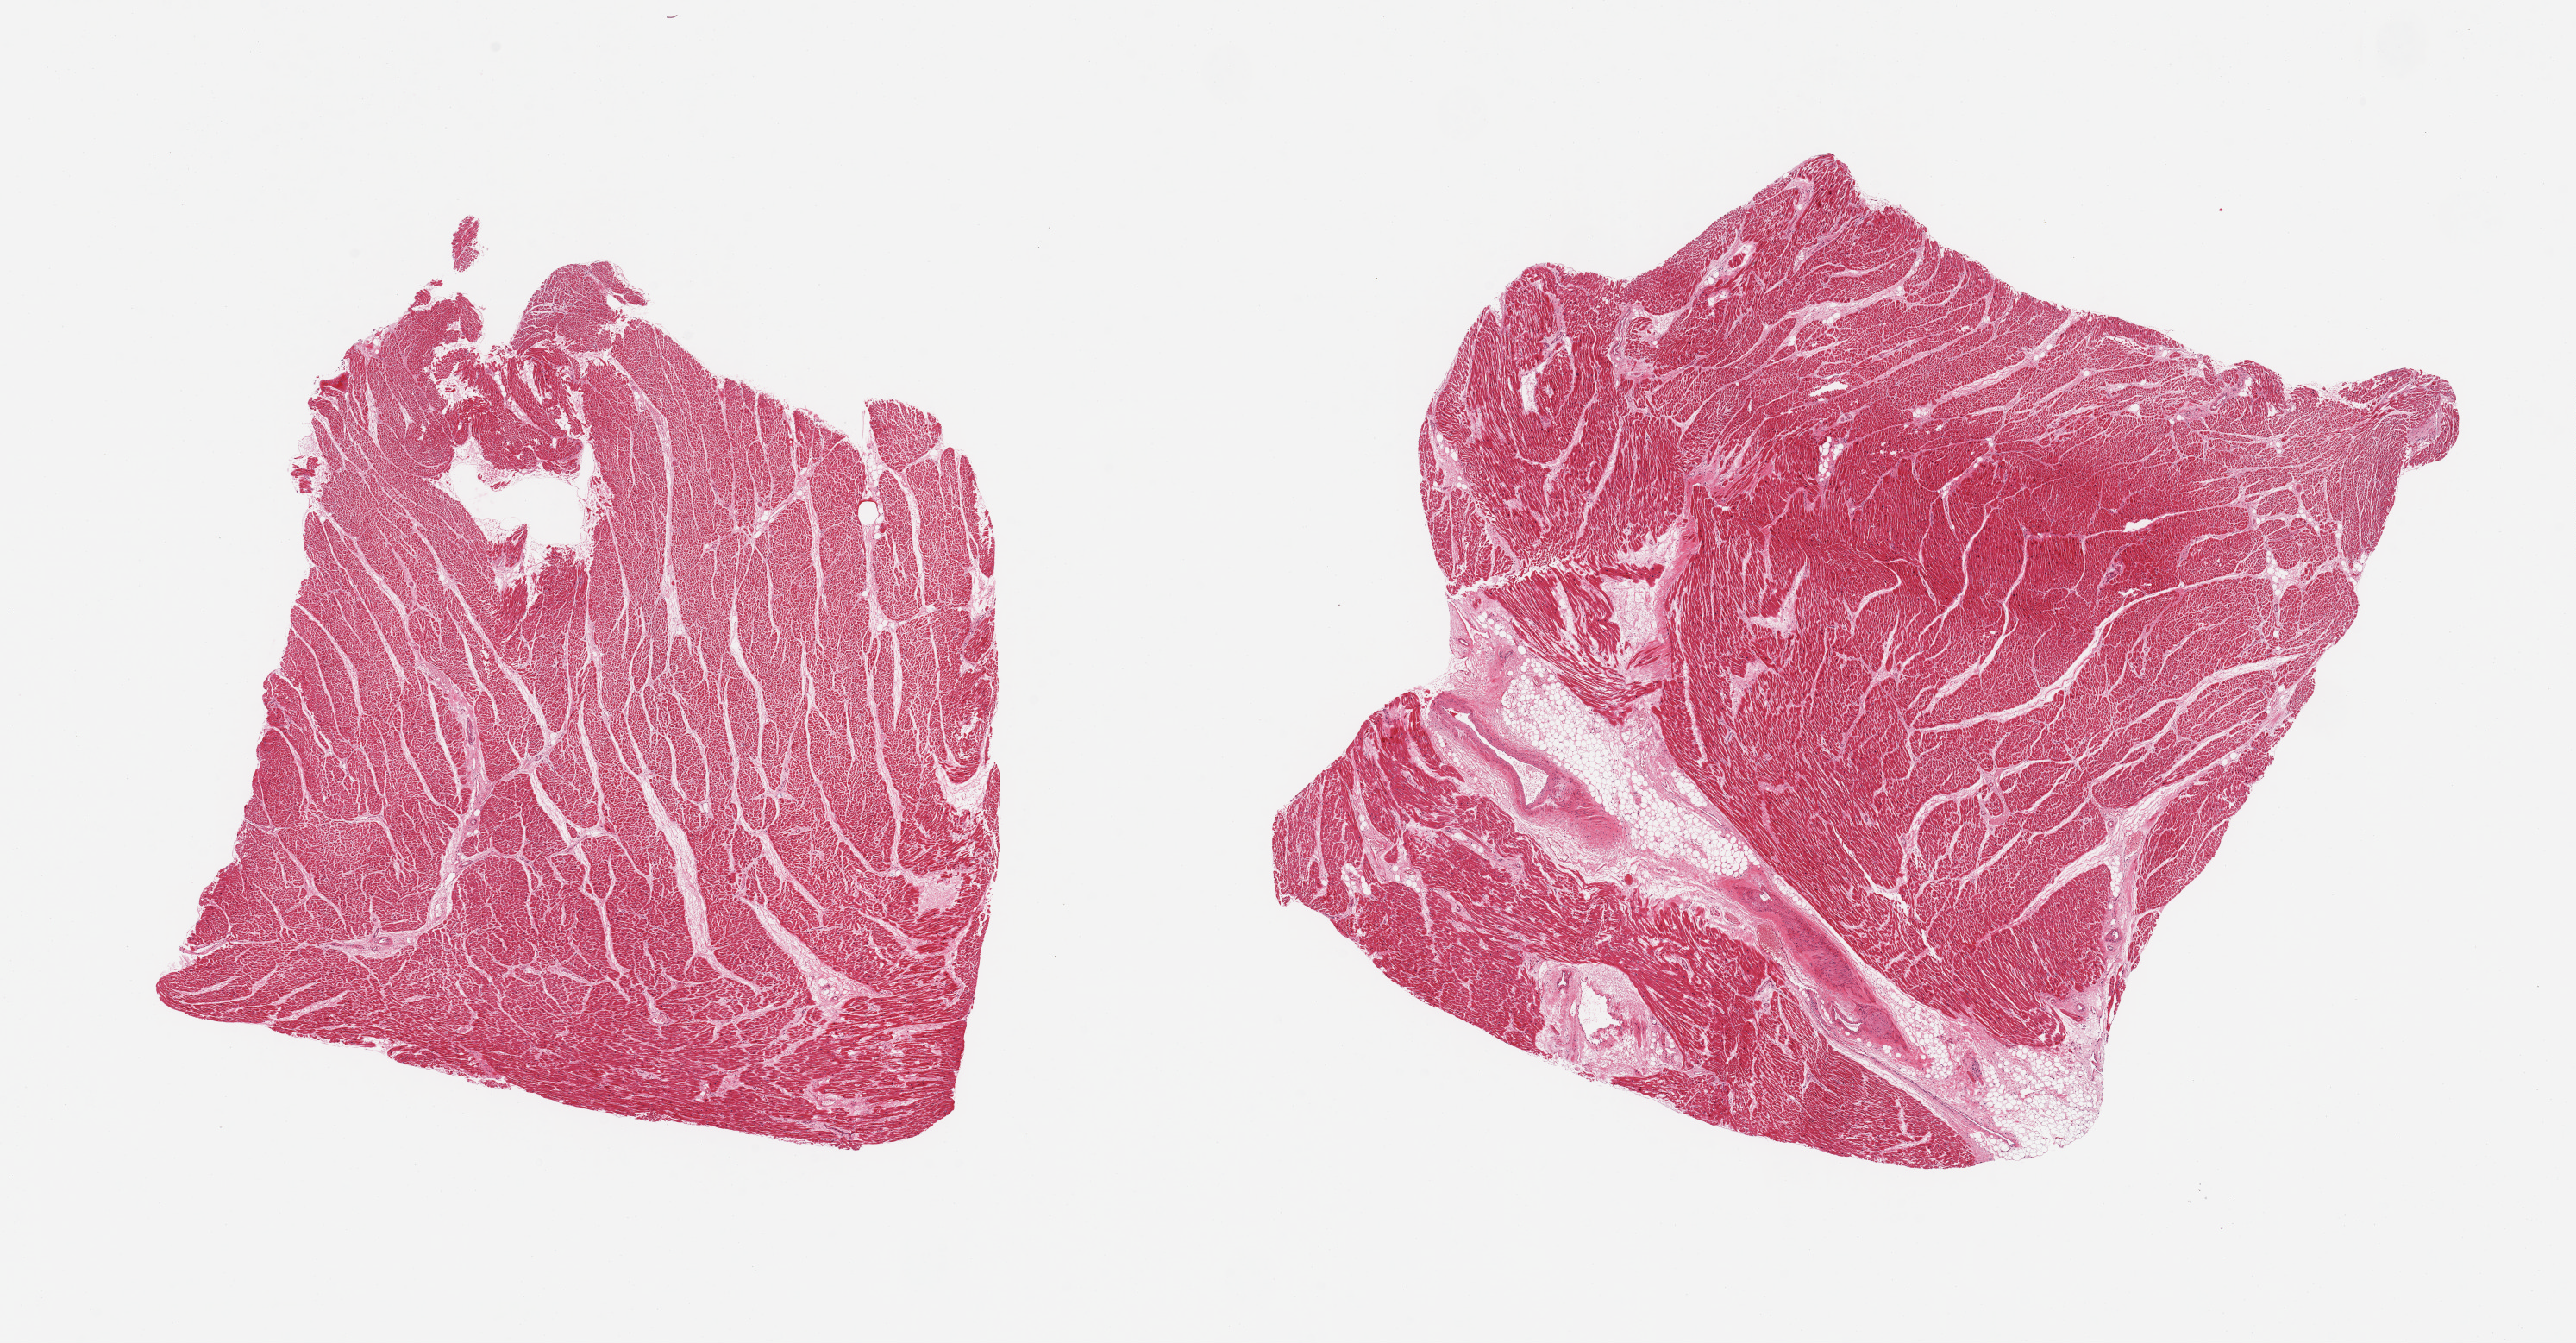
Whole-slide image, haematoxylin and eosin stain, shown as a low-resolution overview of the whole scanned area (about 23.6 x 12.3 mm, slide scanned at 20x). PAXgene-fixed, paraffin-embedded tissue. Sampled site (target tissue): heart. Tissue donor sample. Donor sex: male.
Reviewer comment on this tissue sample: 2 pieces; areas of hypereosinophilia suggest ischemia, but no clear-cut signs of infarction; 10% internal fat in 1 piece.